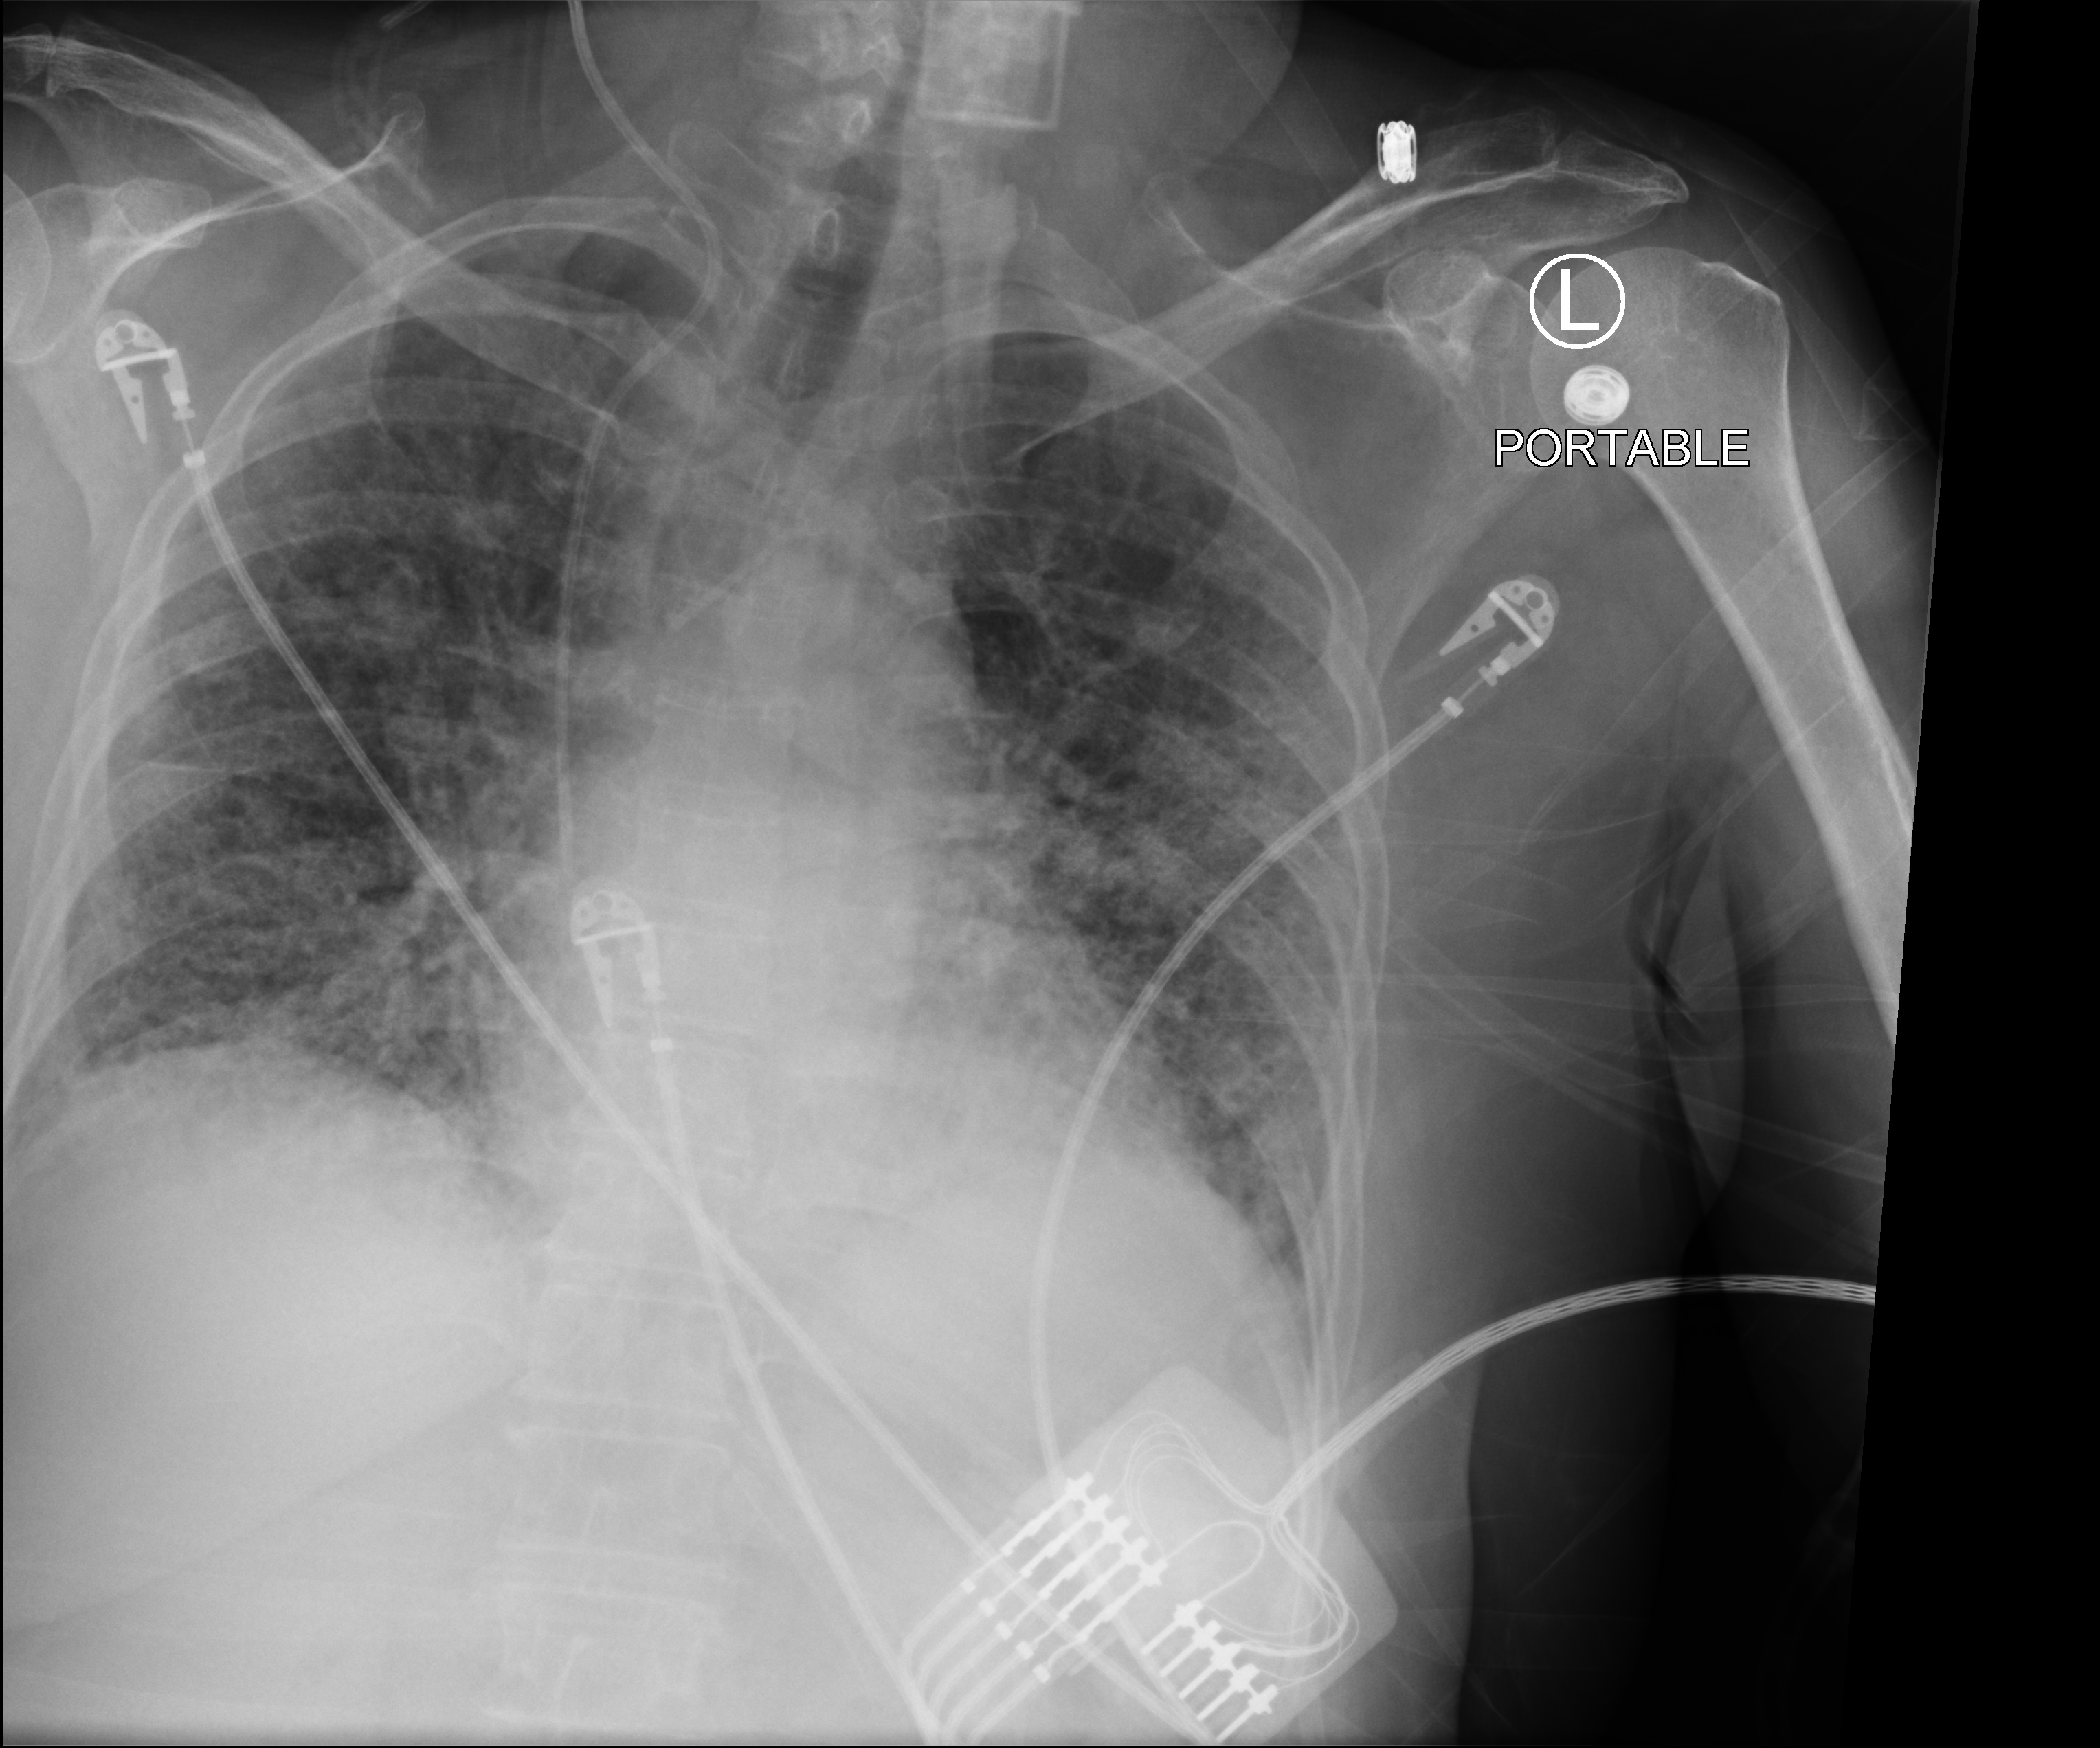
Portable chest radiograph; anteroposterior (AP) projection. Female patient hospitalised with COVID-19, age 60–74 years.
From the hospital-stay record, not from the radiograph (when in the stay this image was taken is not recorded):
- length of hospital stay: 14 days